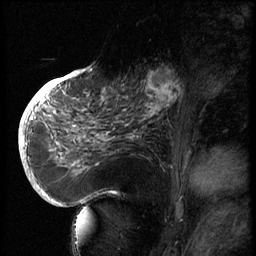
Breast MRI (dynamic contrast-enhanced), one sagittal slice; slice 30 of 66 in the series (ordered by position); 3 images stored at this slice position (order not interpretable as contrast timing); 1.5 T; TE 4.2 ms, TR 8.9 ms; 2.5 mm slice thickness; 256 × 256 image matrix, field of view 200 × 200 mm. Patient: female, 56 years. From the clinical record (not read from this slice): setting: breast cancer imaged before/during neoadjuvant chemotherapy.
Outlined on this slice (semi-automatically segmented with operator editing):
- analysis volume of interest (the breast-tissue region the enhancement analysis was run in; not a lesion): bounding box <129,62,194,127> (left, top, right, bottom; pixels)
- tumour enhancement mask (voxels above the 140 % enhancement threshold inside the analysis volume of interest): <144,67,185,120>